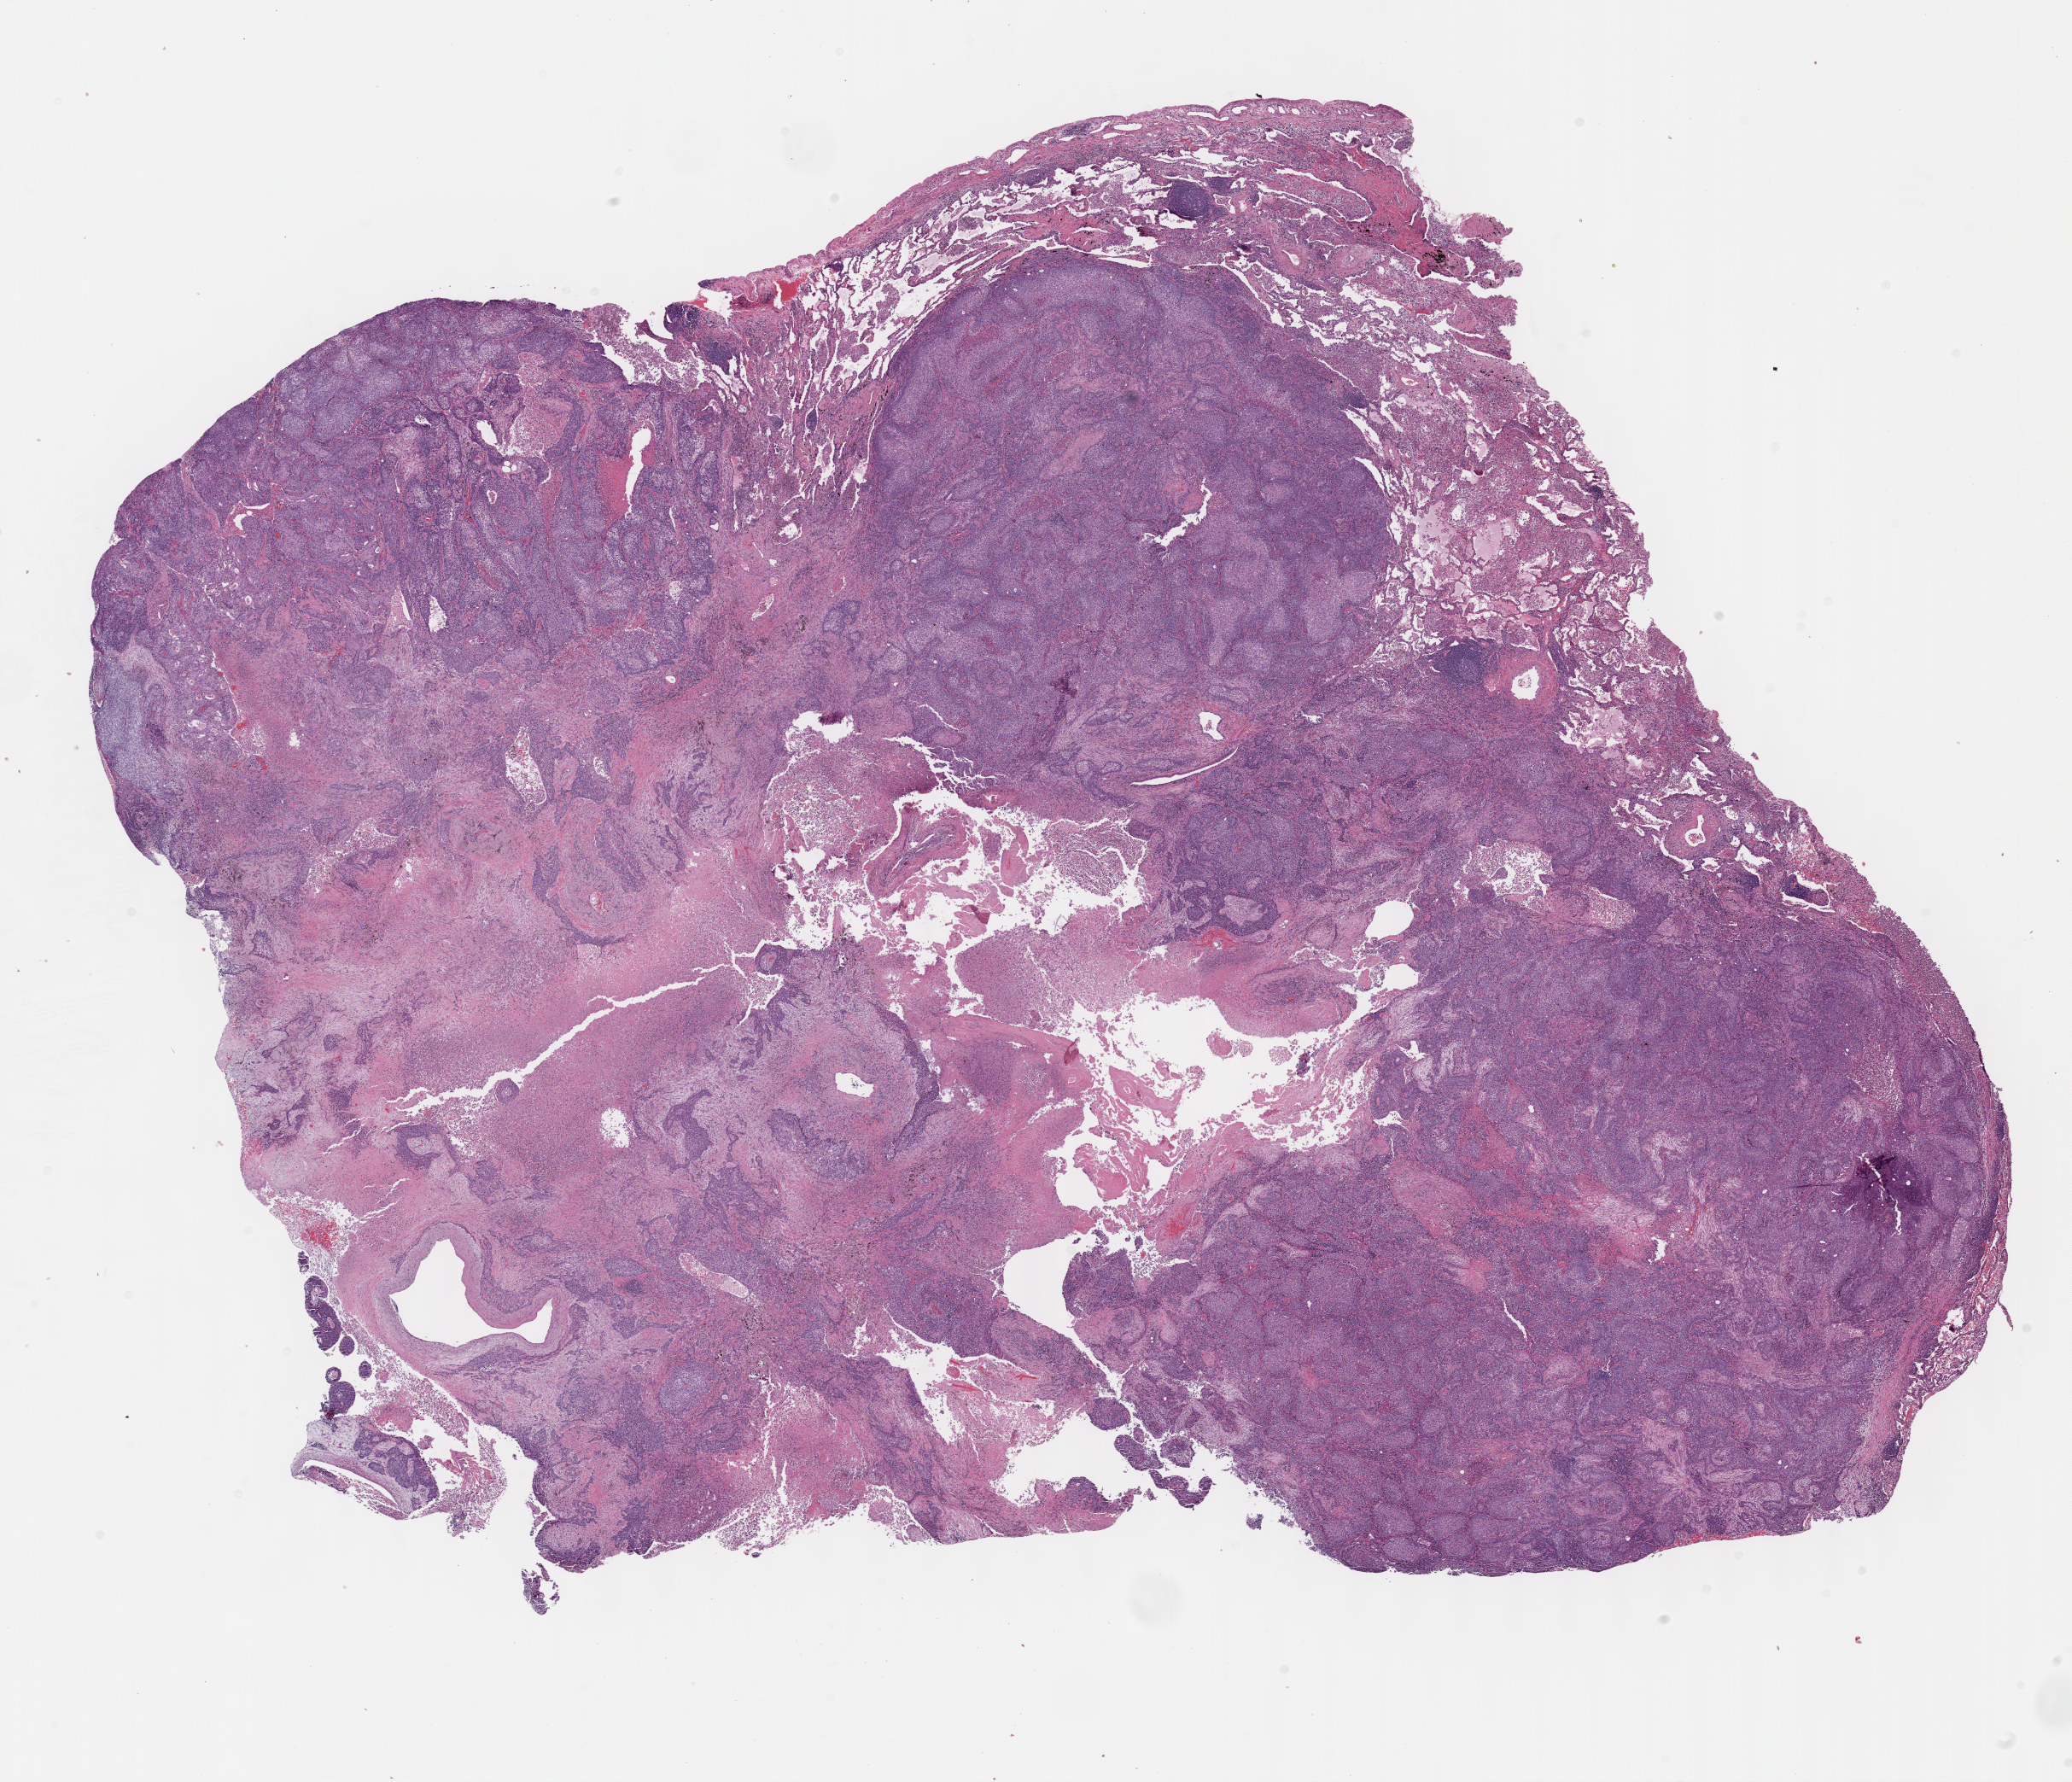
Digitized H&E tissue section (whole slide) — low-resolution overview of the scanned area, about 19.6 x 16.9 mm (from a 40x scan), formalin-fixed paraffin-embedded (FFPE) diagnostic section, sample: primary tumour, lung. Female, age 73 years at initial diagnosis.
- pathologic diagnosis: Squamous cell carcinoma, NOS
- AJCC pathologic stage: IIIA
- TNM: T2a N2 M0